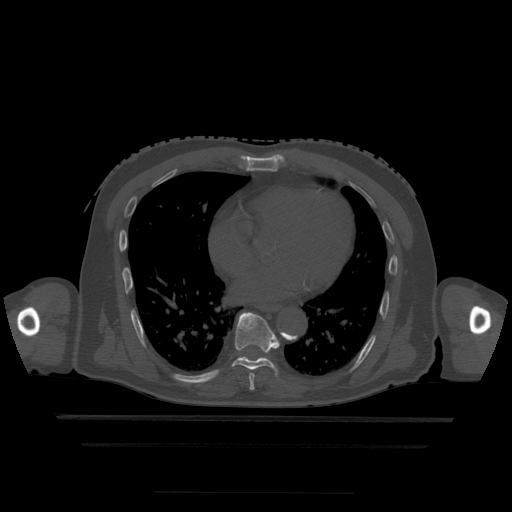
CT including the spine, one axial slice. Bone window (W 1800 / L 400 HU). 512 × 512 image matrix. Patient age 68 years. Case-level facts recorded for this patient, not image findings: primary cancer: urothelial.
Structures marked on this image (semi-automatically segmented with operator editing):
- T7 vertebra: bounding box [x1, y1, x2, y2] px = [249, 373, 255, 392]
- T8 vertebra: [232, 312, 280, 376]
- T9 vertebra: [260, 358, 264, 360]